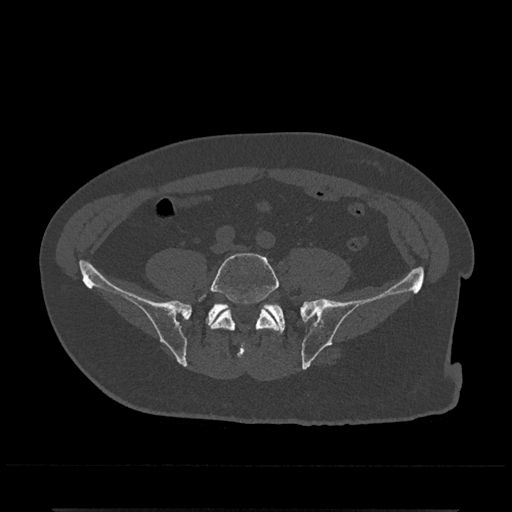
CT including the spine, one axial slice; position 72 of 797 along the scan axis; bone window (W 1800 / L 400 HU); 0.5 mm slice thickness; 512 × 512 image matrix, field of view 393 × 393 mm. Male patient, age 67 years. From the clinical record (not read from this slice): primary cancer: prostate.
Annotated regions visible in this slice (semi-automatically segmented with operator editing):
- L5 vertebra: bounding box <199,253,280,359> (left, top, right, bottom; pixels)